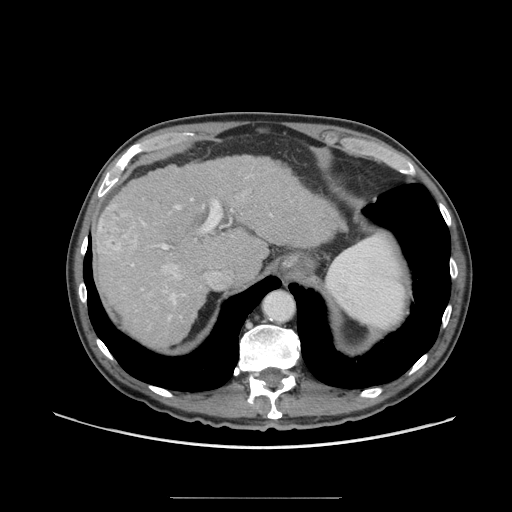
Contrast-enhanced abdominal CT (liver protocol), one axial slice; slice 51 of 71 in the series (ordered by position); reconstruction kernel STANDARD; soft-tissue window (W 400 / L 40 HU); 512 × 512 image matrix, field of view 400 × 400 mm. From the clinical record (not read from this slice): diagnosis: hepatocellular carcinoma (patient treated with transarterial chemoembolisation; whether this scan precedes or follows treatment is not stated here); TNM stage (as recorded): Stage-I; Child-Pugh class: A; tumour differentiation: well differentiated; tumour nodularity: uninodular.
Annotated regions visible in this slice (semi-automatic segmentation, software-assisted and operator-edited):
- abdominal aorta: bounding box <264,292,294,321> (left, top, right, bottom; pixels)
- liver parenchyma outside the tumour (the mass and vessels are separate outlines, so this box may not span the whole liver): <94,154,338,346>
- mass: <94,203,144,263>
- liver vessels: <131,198,272,320>